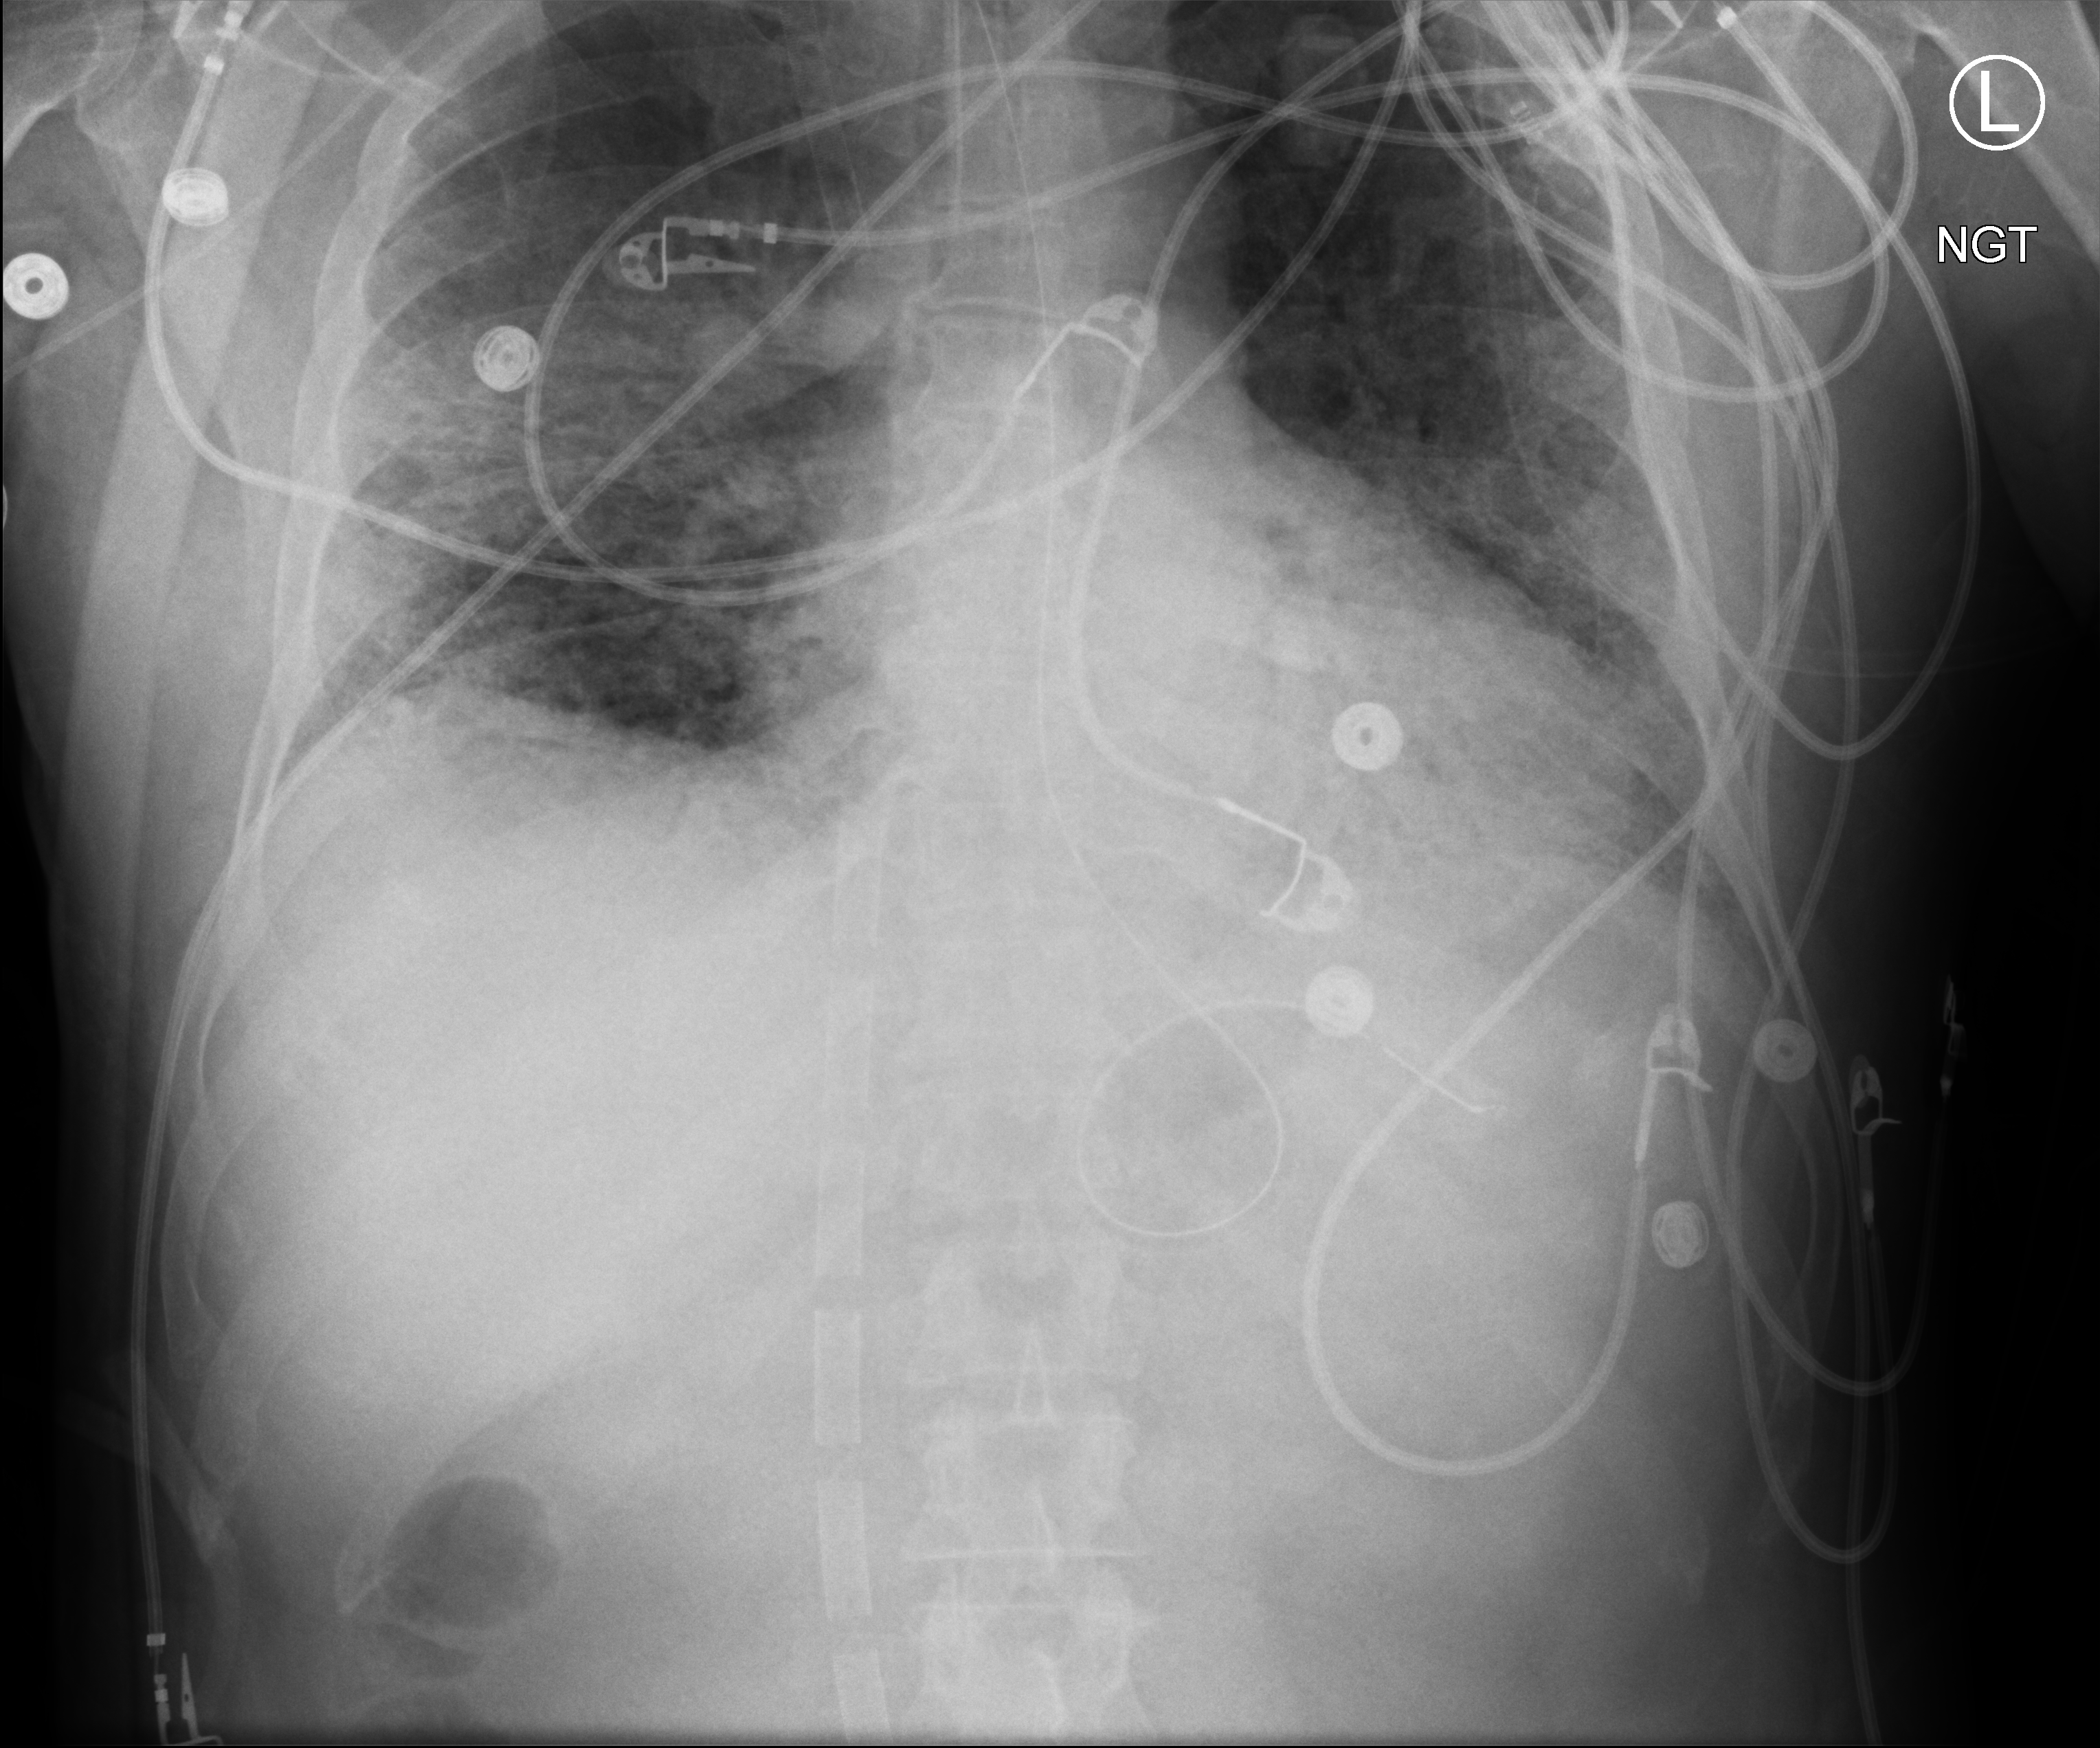
Bedside chest radiograph (computed radiography). Male patient hospitalised with COVID-19, age 18–59 years.
Admission-level facts for this patient (not findings on this image; timing relative to this image not recorded): smoking status (admission record): never.